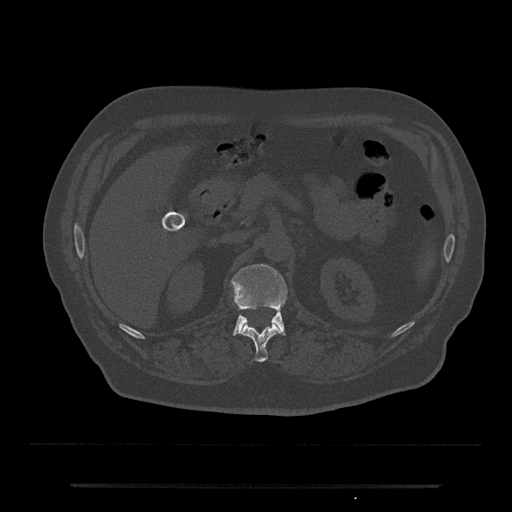
CT including the spine, one axial slice. Position 563 of 797 along the scan axis. Reconstruction kernel Br40s/3. 120 kVp. Bone window (W 1800 / L 400 HU). 512 × 512 image matrix, field of view 434 × 434 mm. Male patient, age 80 years. From the clinical record (not read from this slice): primary cancer: prostate.
Annotated regions visible in this slice (semi-automatically segmented with operator editing):
- L1 vertebra: box from (x=231, y=264) to (x=288, y=336) px
- T12 vertebra: (x=242, y=324)–(x=281, y=362)